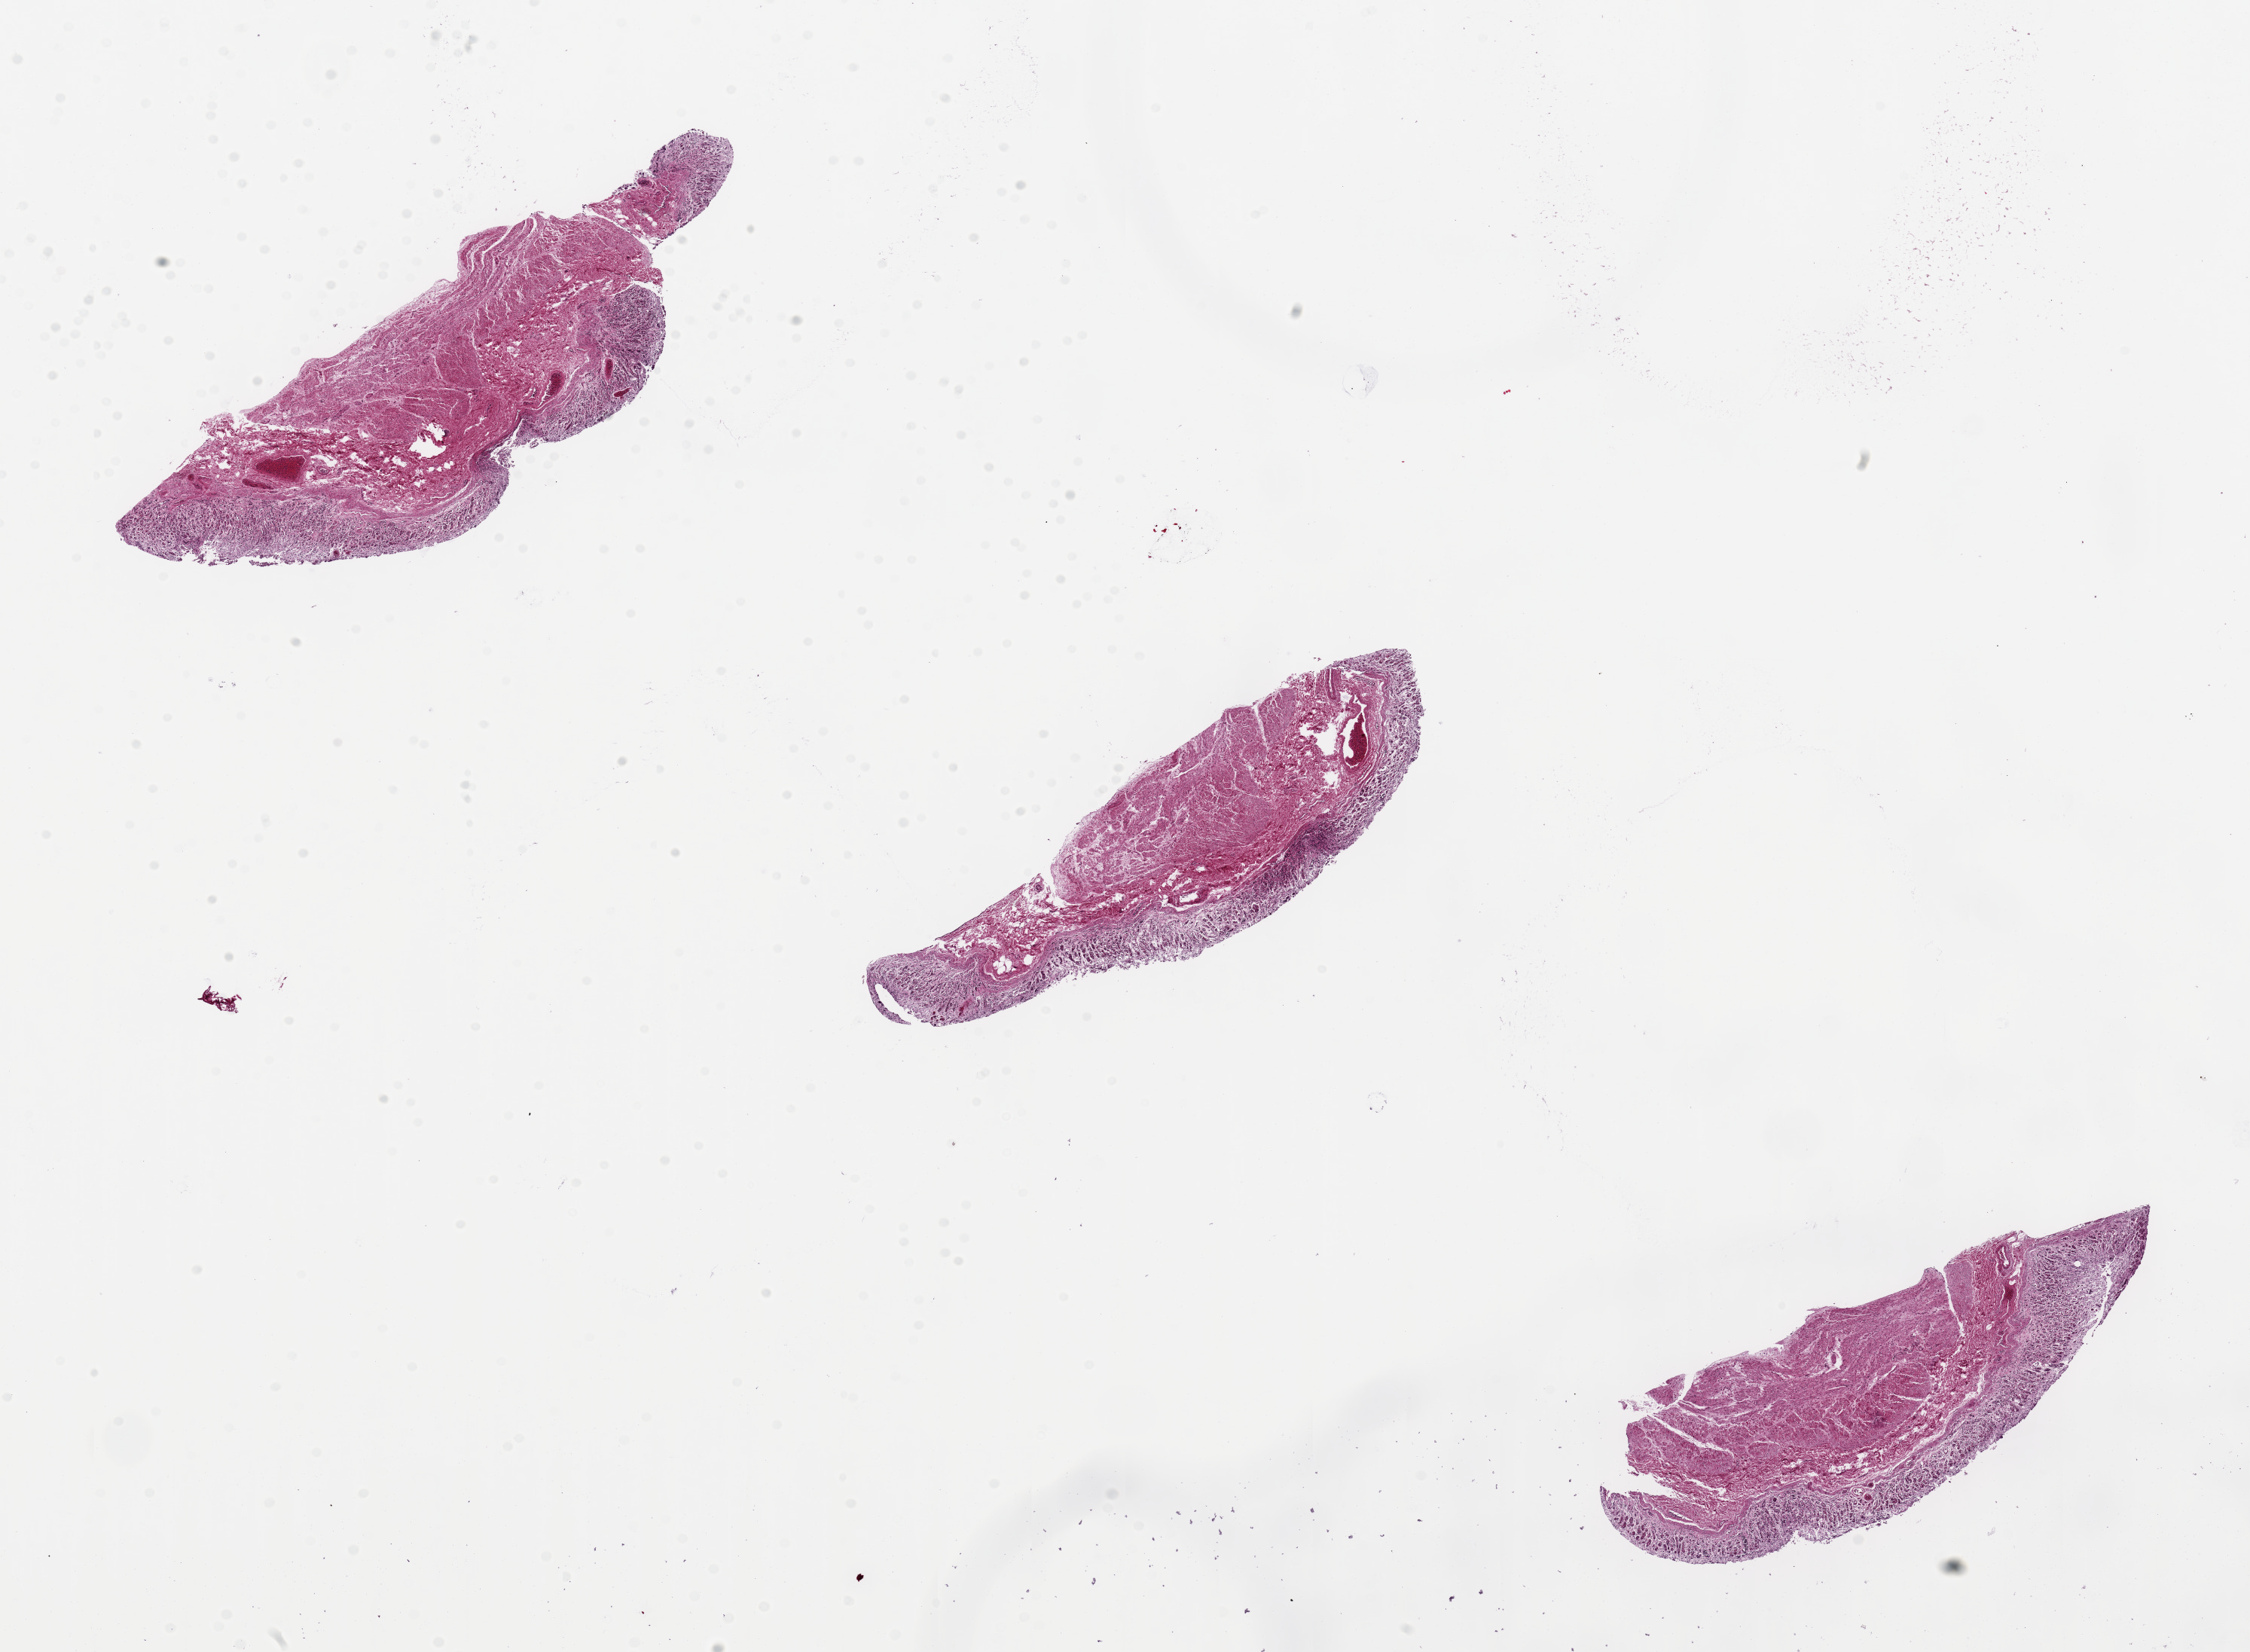
Digitized haematoxylin and eosin-stained section — shown as a low-resolution overview of the whole scanned area (about 23.6 x 17.3 mm); PAXgene-fixed, paraffin-embedded tissue; sampled site (target tissue): stomach; donor tissue sample. Donor: male.
Review note (as recorded): 3 ~6.5mm pieces; mucosa is ~20-25% of specimen thickness.